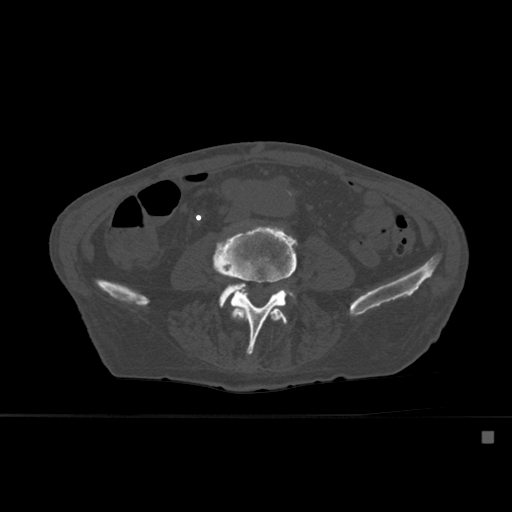
CT including the spine, one axial slice; slice 193 of 527 in the series (ordered by position); bone window (W 1800 / L 400 HU); 1.5 mm slice thickness; 512 × 512 image matrix. Patient: male, 78 years. From the clinical record (not read from this slice): primary cancer: prostate.
Structures marked on this image (semi-automatic segmentation, software-assisted and operator-edited):
- L3 vertebra: bounding box (x1, y1, x2, y2) in pixels: (230, 308, 288, 325)
- L4 vertebra: (213, 227, 297, 356)
- L5 vertebra: (219, 283, 296, 306)